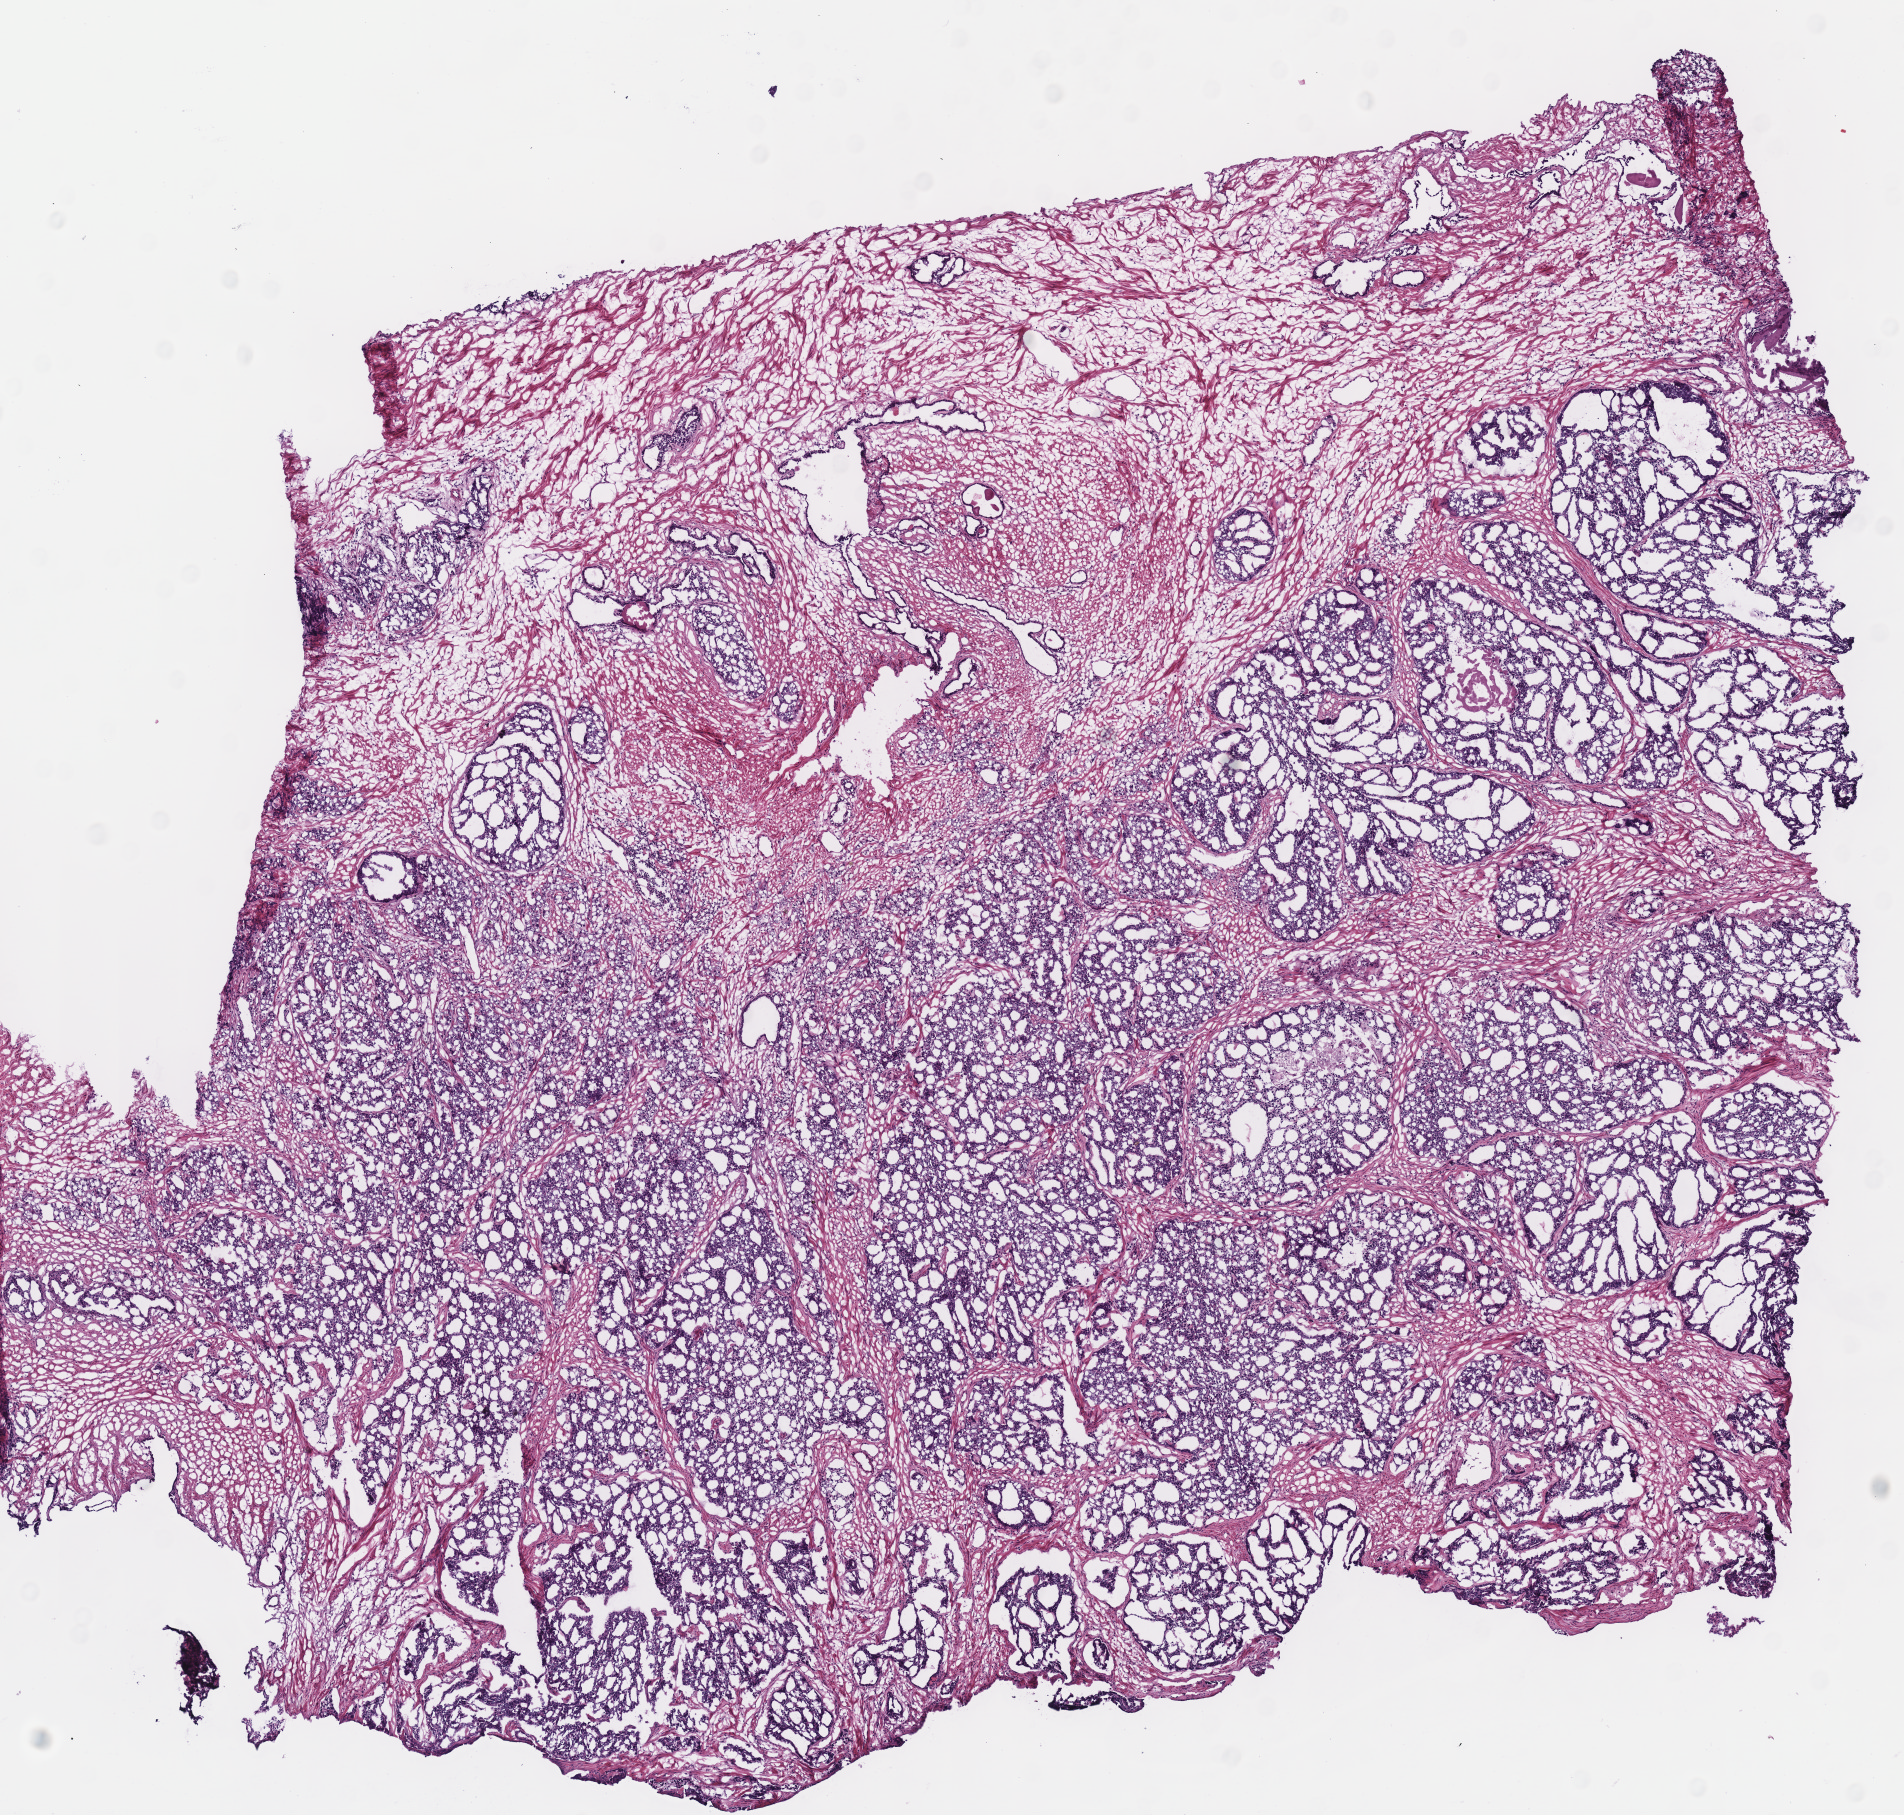
H&E whole-slide image — whole scanned area (about 7.5 x 7.1 mm) shown as a low-resolution overview; frozen section from the top of the tissue portion; sample: primary tumour, prostate. Male patient; age at initial diagnosis 63 years. Gleason score: 8 (4+4). Slide review estimates, as recorded: tumour cells 70%, tumour nuclei 90%, normal cells 10%, stromal cells 18%, necrosis 2%. Infiltration values recorded for this section: lymphocyte infiltration 1%, monocyte infiltration 0%, neutrophil infiltration 0%.
- histologic diagnosis: Acinar cell carcinoma (prostate gland)